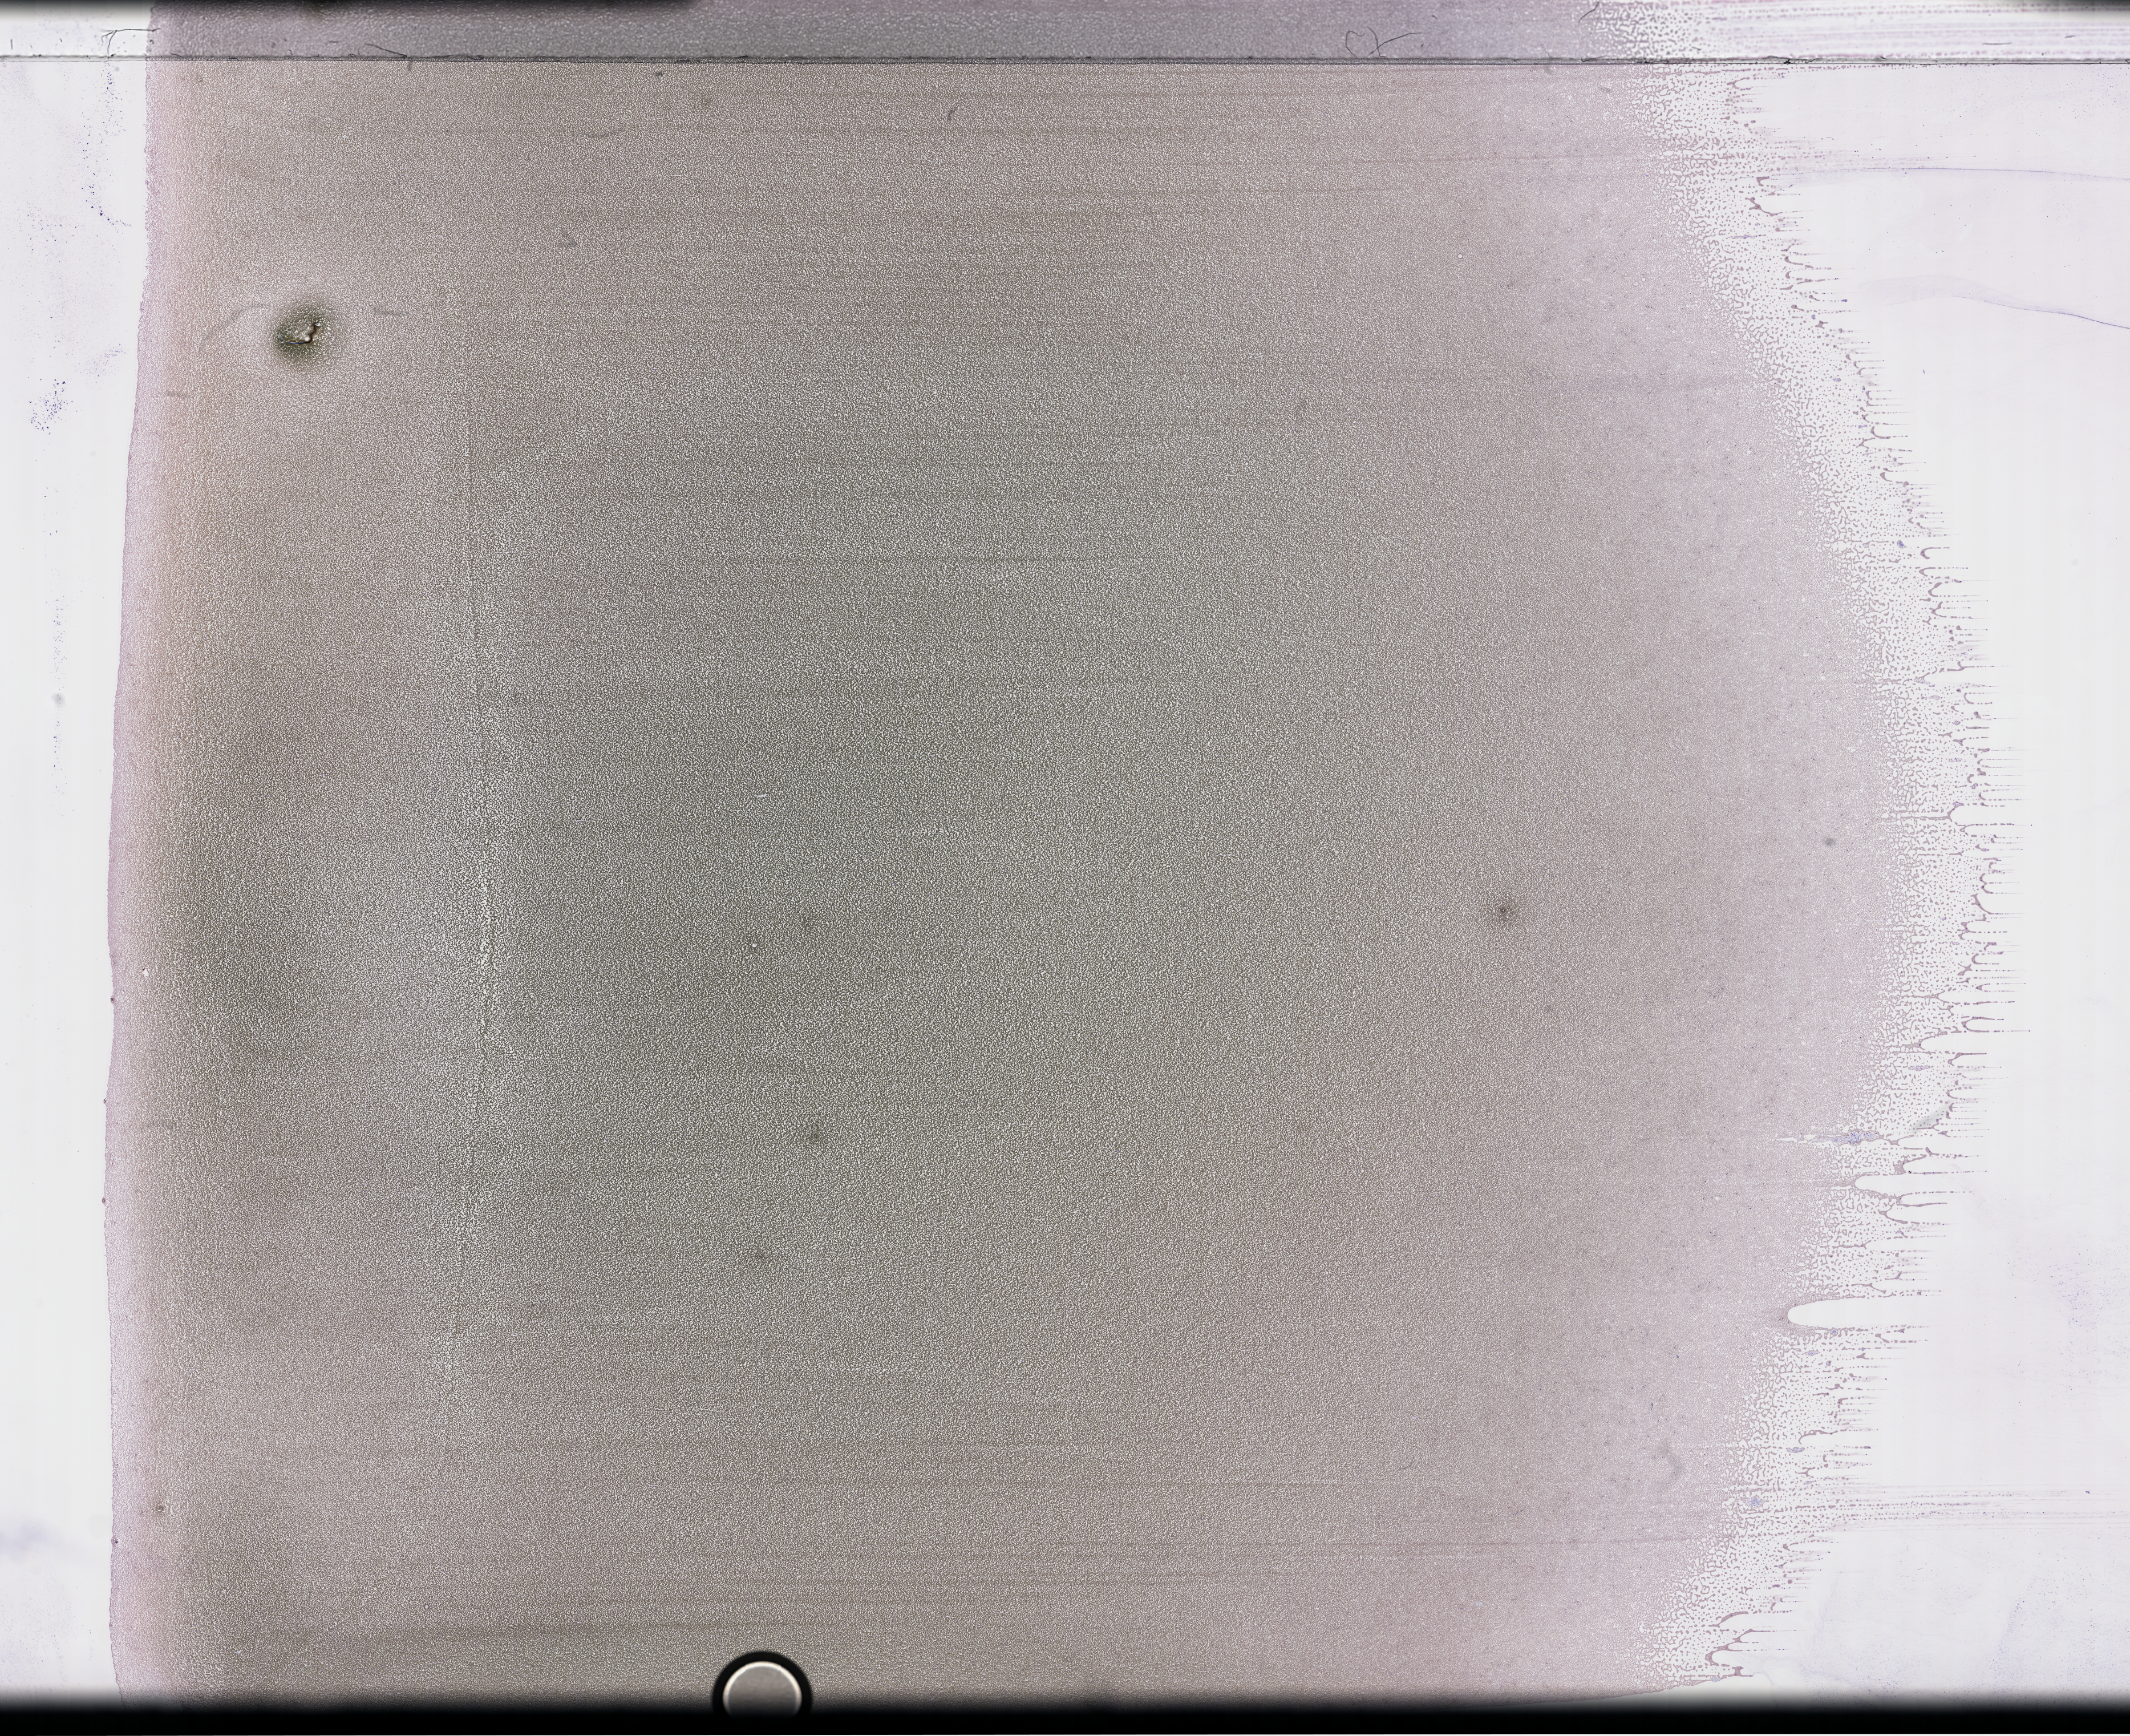
Wright–Giemsa-stained whole blood smear, whole-slide image — a low-resolution overview of the entire scanned area, about 30.2 x 24.6 mm. Smear from an EDTA sample. Specimen time point: collected on treatment. Patient: female.
From a patient with: Plasma Cell Myeloma.